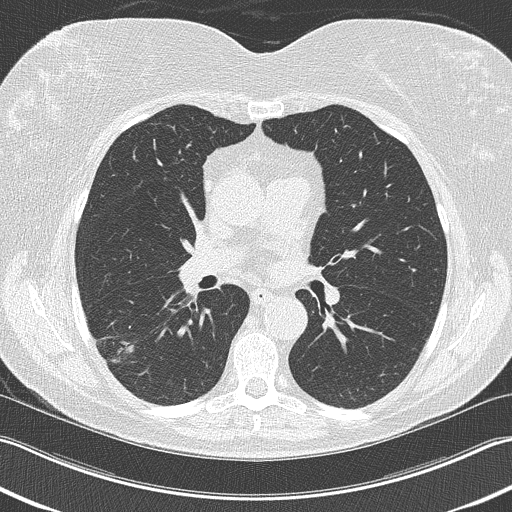
Low-dose screening chest CT, one axial slice; slice 126 of 210 in the series (ordered by position); 120 kVp; lung window (W 1500 / L -600 HU); 2 mm slice thickness; 512 × 512 image matrix.
Outlined on this slice (manually delineated by an expert):
- lesion 1 (tumor, lower lobe of right lung): box from (x=113, y=341) to (x=134, y=363) px